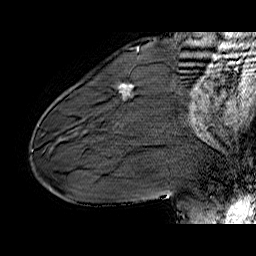
Breast MRI (dynamic contrast-enhanced), one sagittal slice; slice 21 of 60 in the series (ordered by position); dynamic contrast-enhanced series, time point 2 of 6 at this slice position (early post-contrast); 1.5 T; TE 6.4 ms, TR 32.9 ms; 256 × 256 image matrix, field of view 200 × 200 mm. Female patient. From the clinical record (not read from this slice): setting: breast cancer imaged before/during neoadjuvant chemotherapy; receptor status: HER2-positive.
Structures marked on this image (semi-automatic segmentation, software-assisted and operator-edited):
- analysis volume of interest (the breast-tissue region the enhancement analysis was run in; not a lesion): bounding box (x1, y1, x2, y2) in pixels: (118, 84, 132, 101)
- tumour enhancement mask (voxels above the 100 % enhancement threshold inside the analysis volume of interest): (122, 84, 132, 87)